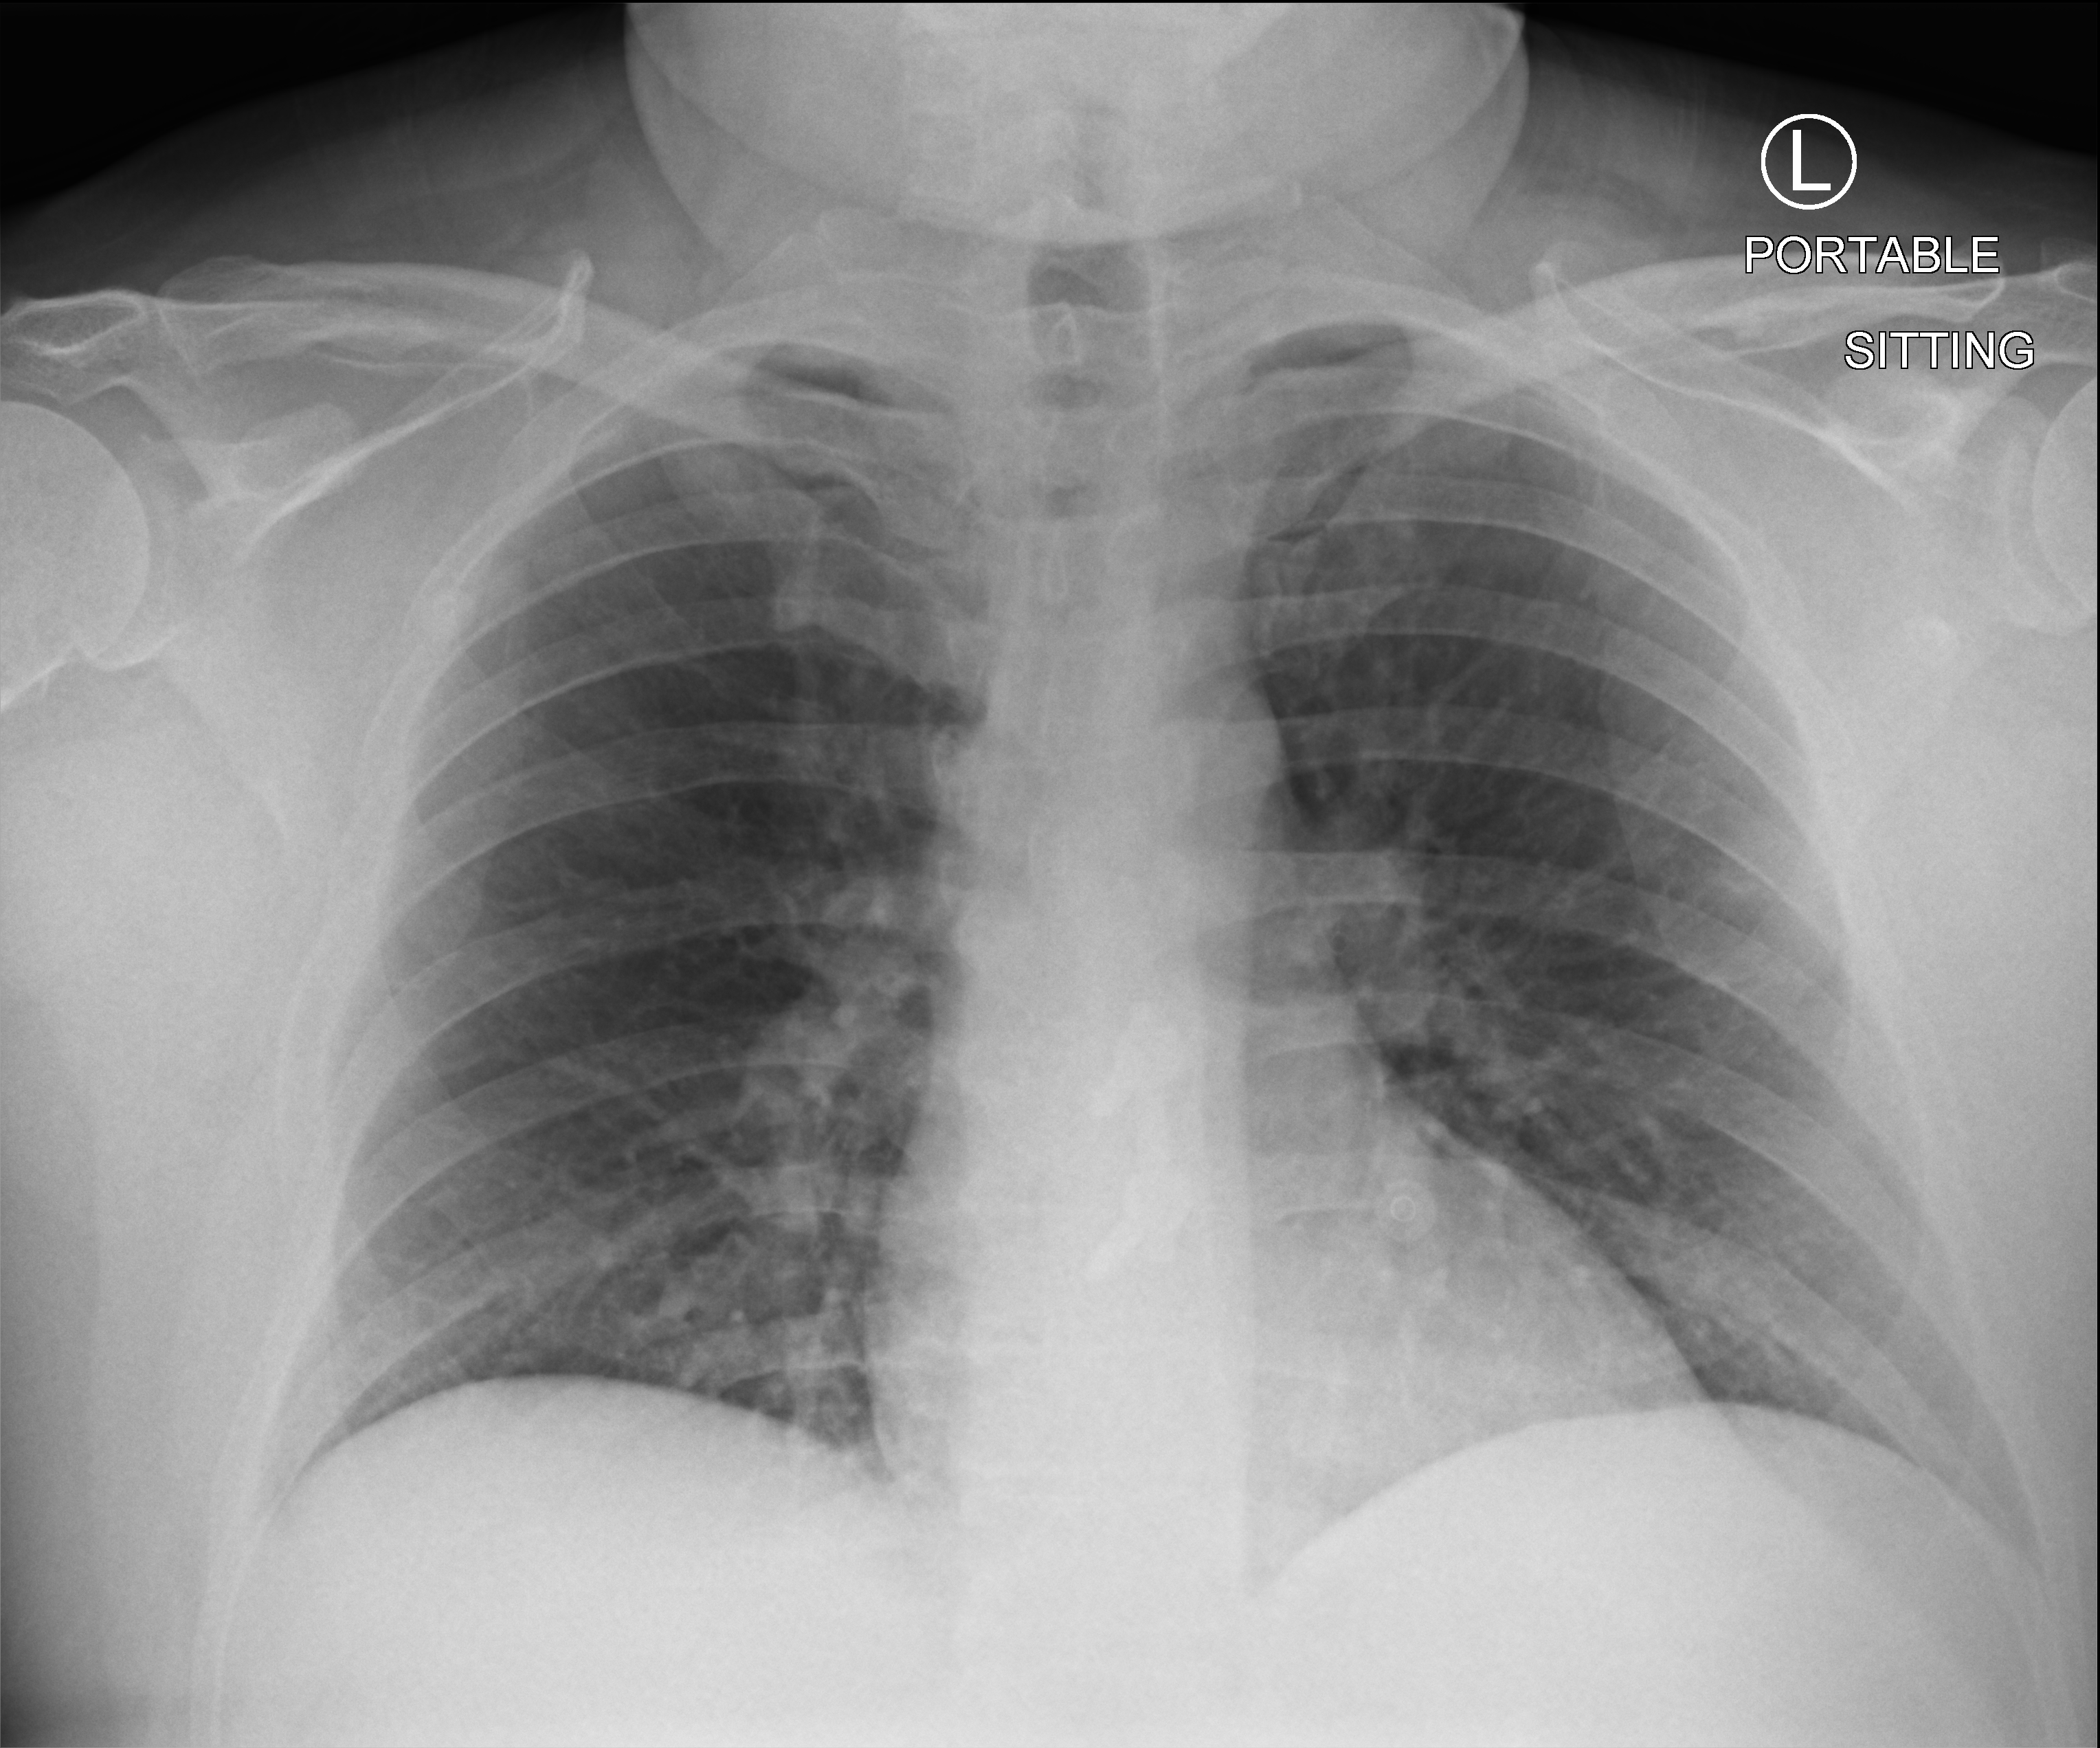
Bedside chest radiograph (computed radiography); anteroposterior (AP) projection. Patient hospitalised with COVID-19; male, aged 18–59 years.
Admission-level facts for this patient (not findings on this image; timing relative to this image not recorded): admitted to intensive care during this hospital stay: no; mechanically ventilated during this hospital stay: no.